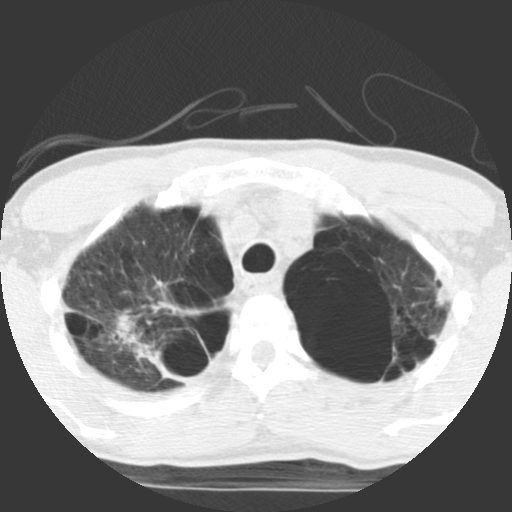
Axial slice from a low-dose chest CT screening exam; baseline annual screen; lung window (W 1500 / L -600 HU); 2.5 mm slice thickness; 512 × 512 image matrix. Male, age 62 years at enrolment. Current smoker at enrolment.
Lesion marked by an expert reader, bounding box [x1, y1, x2, y2] px = [115, 314, 213, 390]. No non-calcified nodule or mass ≥4 mm was recorded by the screening reader at this exam. Lung cancer was diagnosed 357 days after this screen (after the second annual screen): non-small cell carcinoma, right upper lobe, poorly differentiated (G3), stage IA (AJCC 6th edition), 70 mm at pathology.